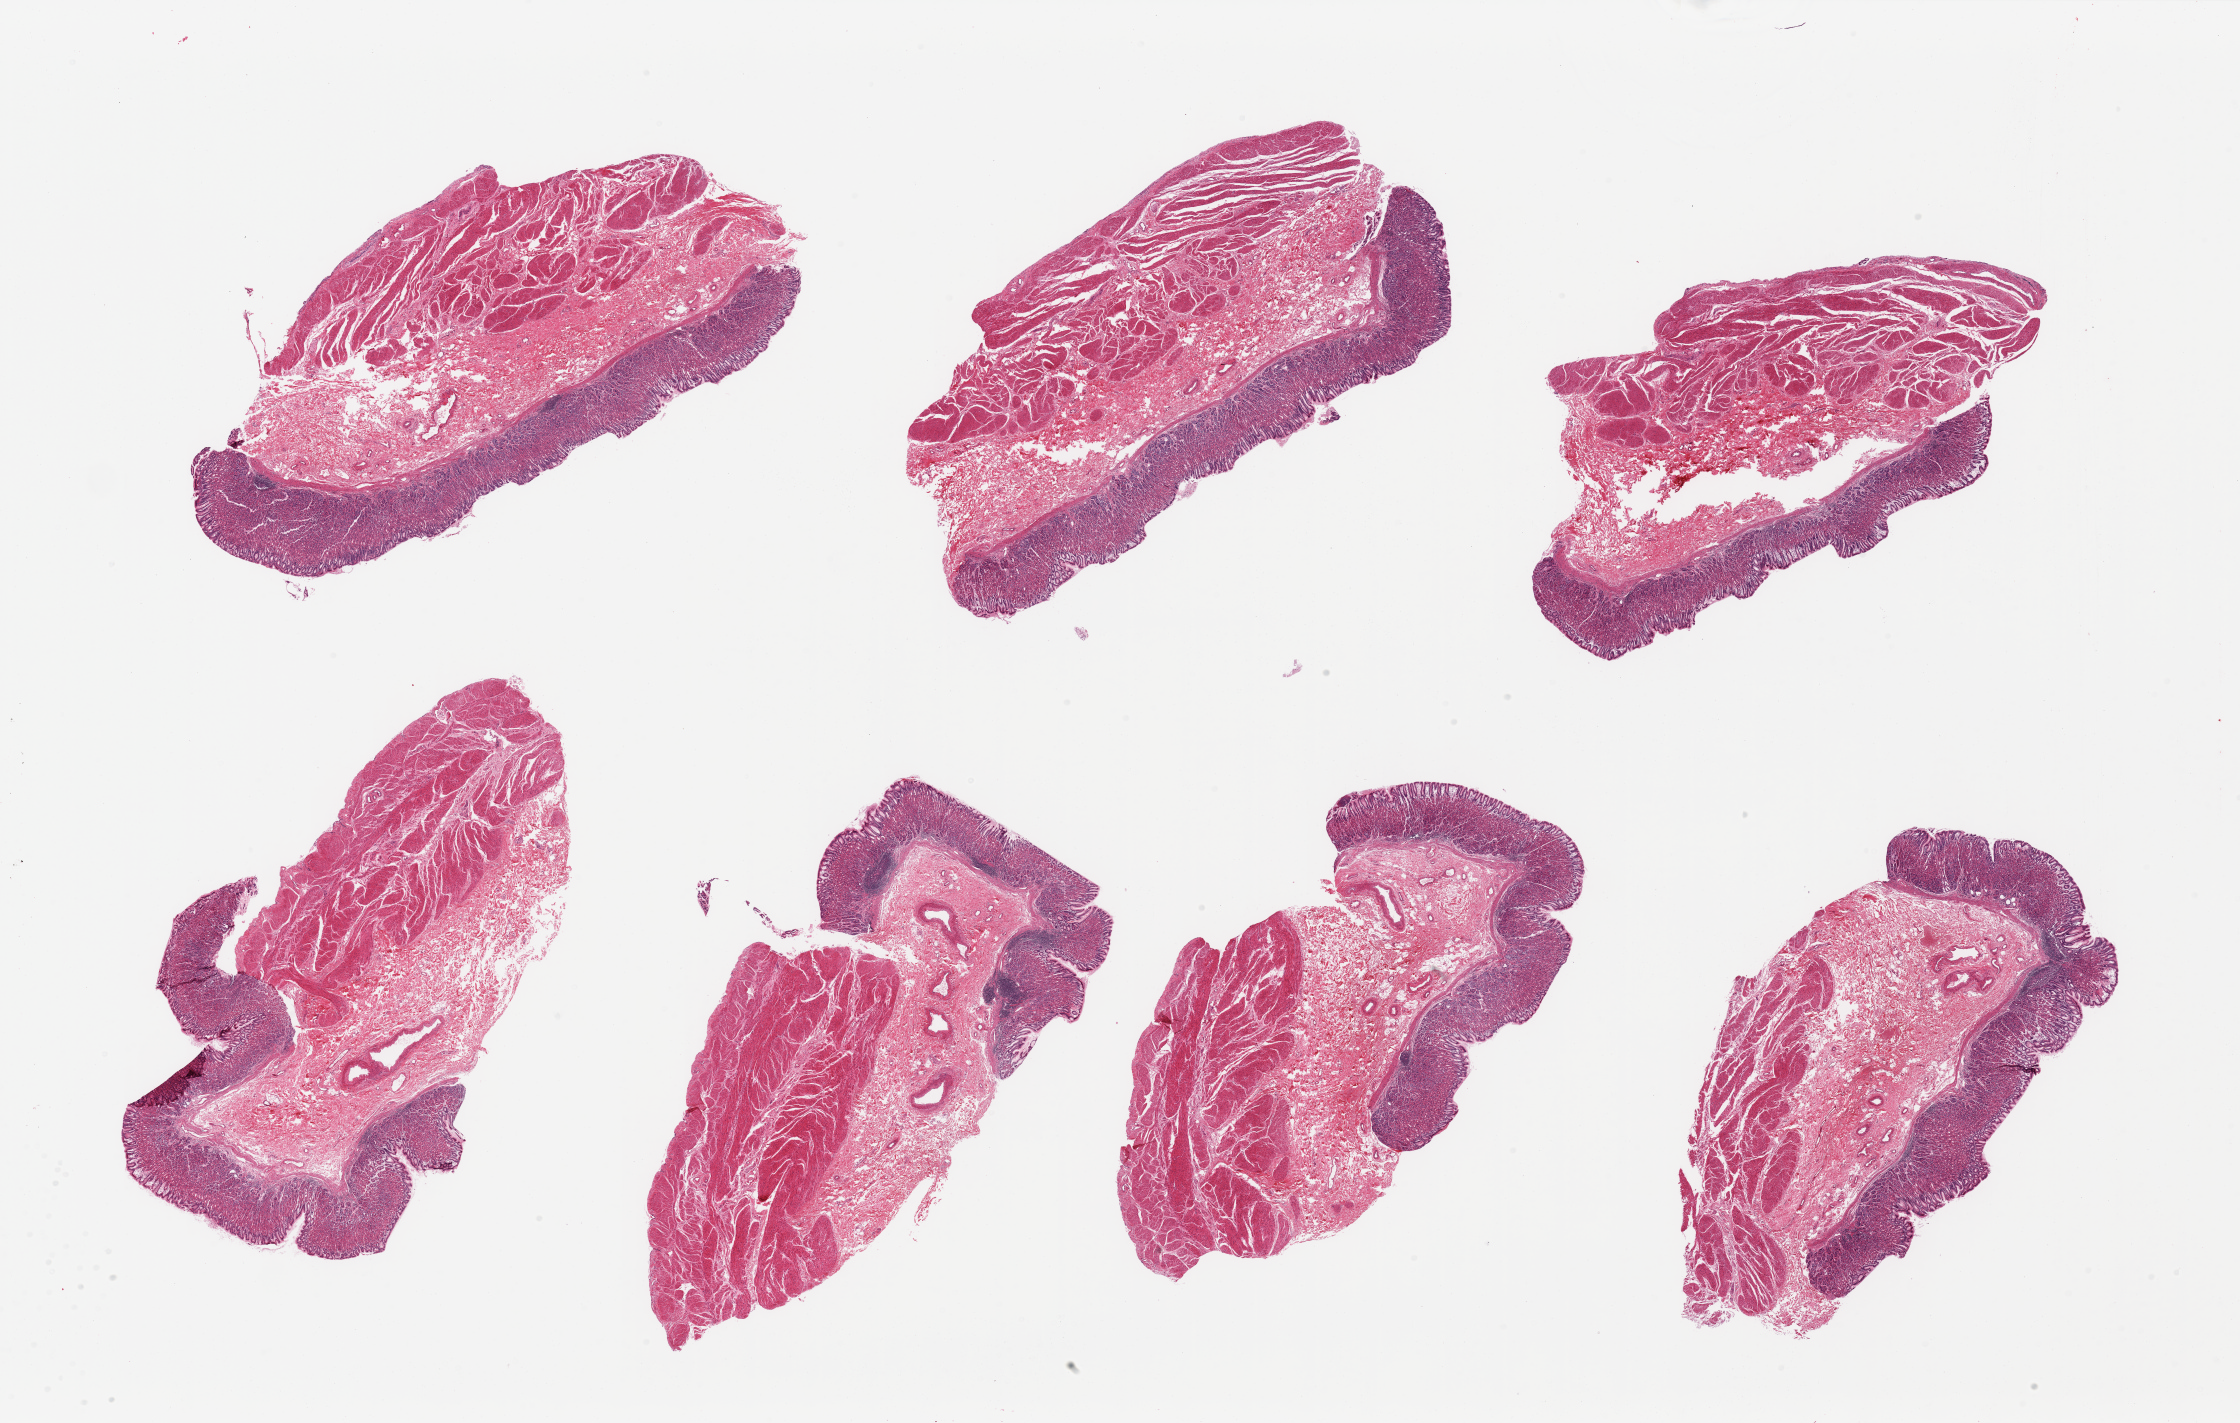
Whole-slide image, hematoxylin and eosin (H&E) stain, low-resolution overview of the scanned area, about 35.4 x 22.5 mm (from a 20x scan); PAXgene-fixed, paraffin-embedded tissue; sampled site (target tissue): stomach; donor tissue sample.
Pathologist's review note for this sample: 7 pieces; mild to moderate autolysis of mucosa and moderate autolysis of submucosa; preserved muscularis; scattered lymphoid aggregates in submucosa.